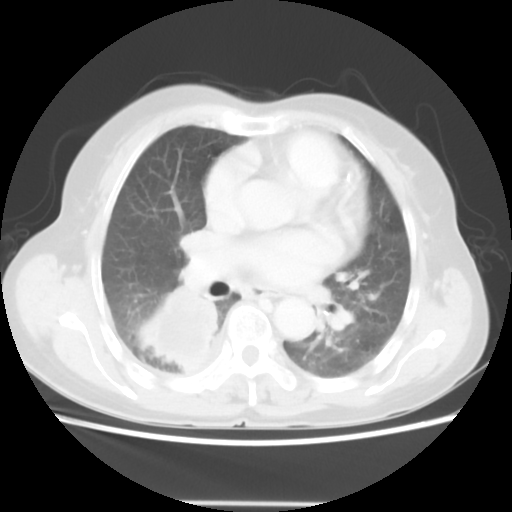
Chest CT, one axial slice; position 27 of 52 along the scan axis; lung window (W 1500 / L -600 HU); 512 × 512 image matrix, field of view 337 × 337 mm. Patient: female, 67 years. Case-level facts recorded for this patient, not image findings: clinical TNM (as recorded): T3 N1 M1.
Structures marked on this image (bounding box drawn by a radiologist):
- lung tumour (recorded histology: adenocarcinoma): bounding box (x1, y1, x2, y2) in pixels: (139, 283, 227, 370)